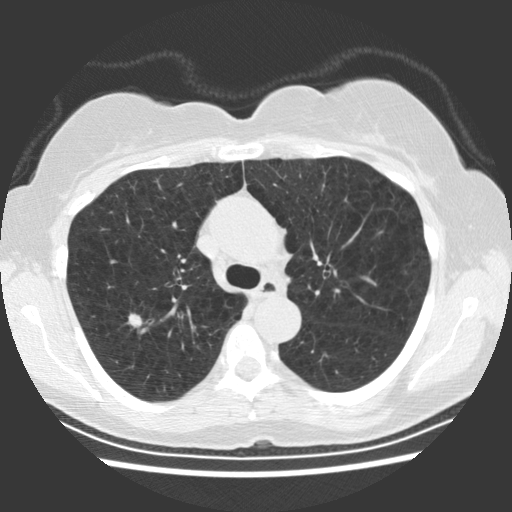
Low-dose screening chest CT, axial slice. First (baseline) screen. Lung window (W 1500 / L -600 HU). 2.5 mm slice thickness. Standard (soft-tissue) reconstruction kernel (STANDARD). 120 kVp. Female participant, aged 66 years at enrolment. Former smoker at enrolment.
Lesion marked by an expert reader, bounding box [x1, y1, x2, y2] px = [111, 301, 153, 340]. Screening reader's record for this exam (one nodule recorded; not confirmed to be the boxed lesion): non-calcified nodule or mass ≥4 mm, right upper lobe, 10 × 8 mm, smooth margins, soft tissue attenuation. Participant outcome: lung cancer diagnosed 54 days after this screen — squamous cell carcinoma, keratinizing, NOS, right upper lobe, poorly differentiated (G3), stage IA (AJCC 6th edition), 11 mm at pathology.